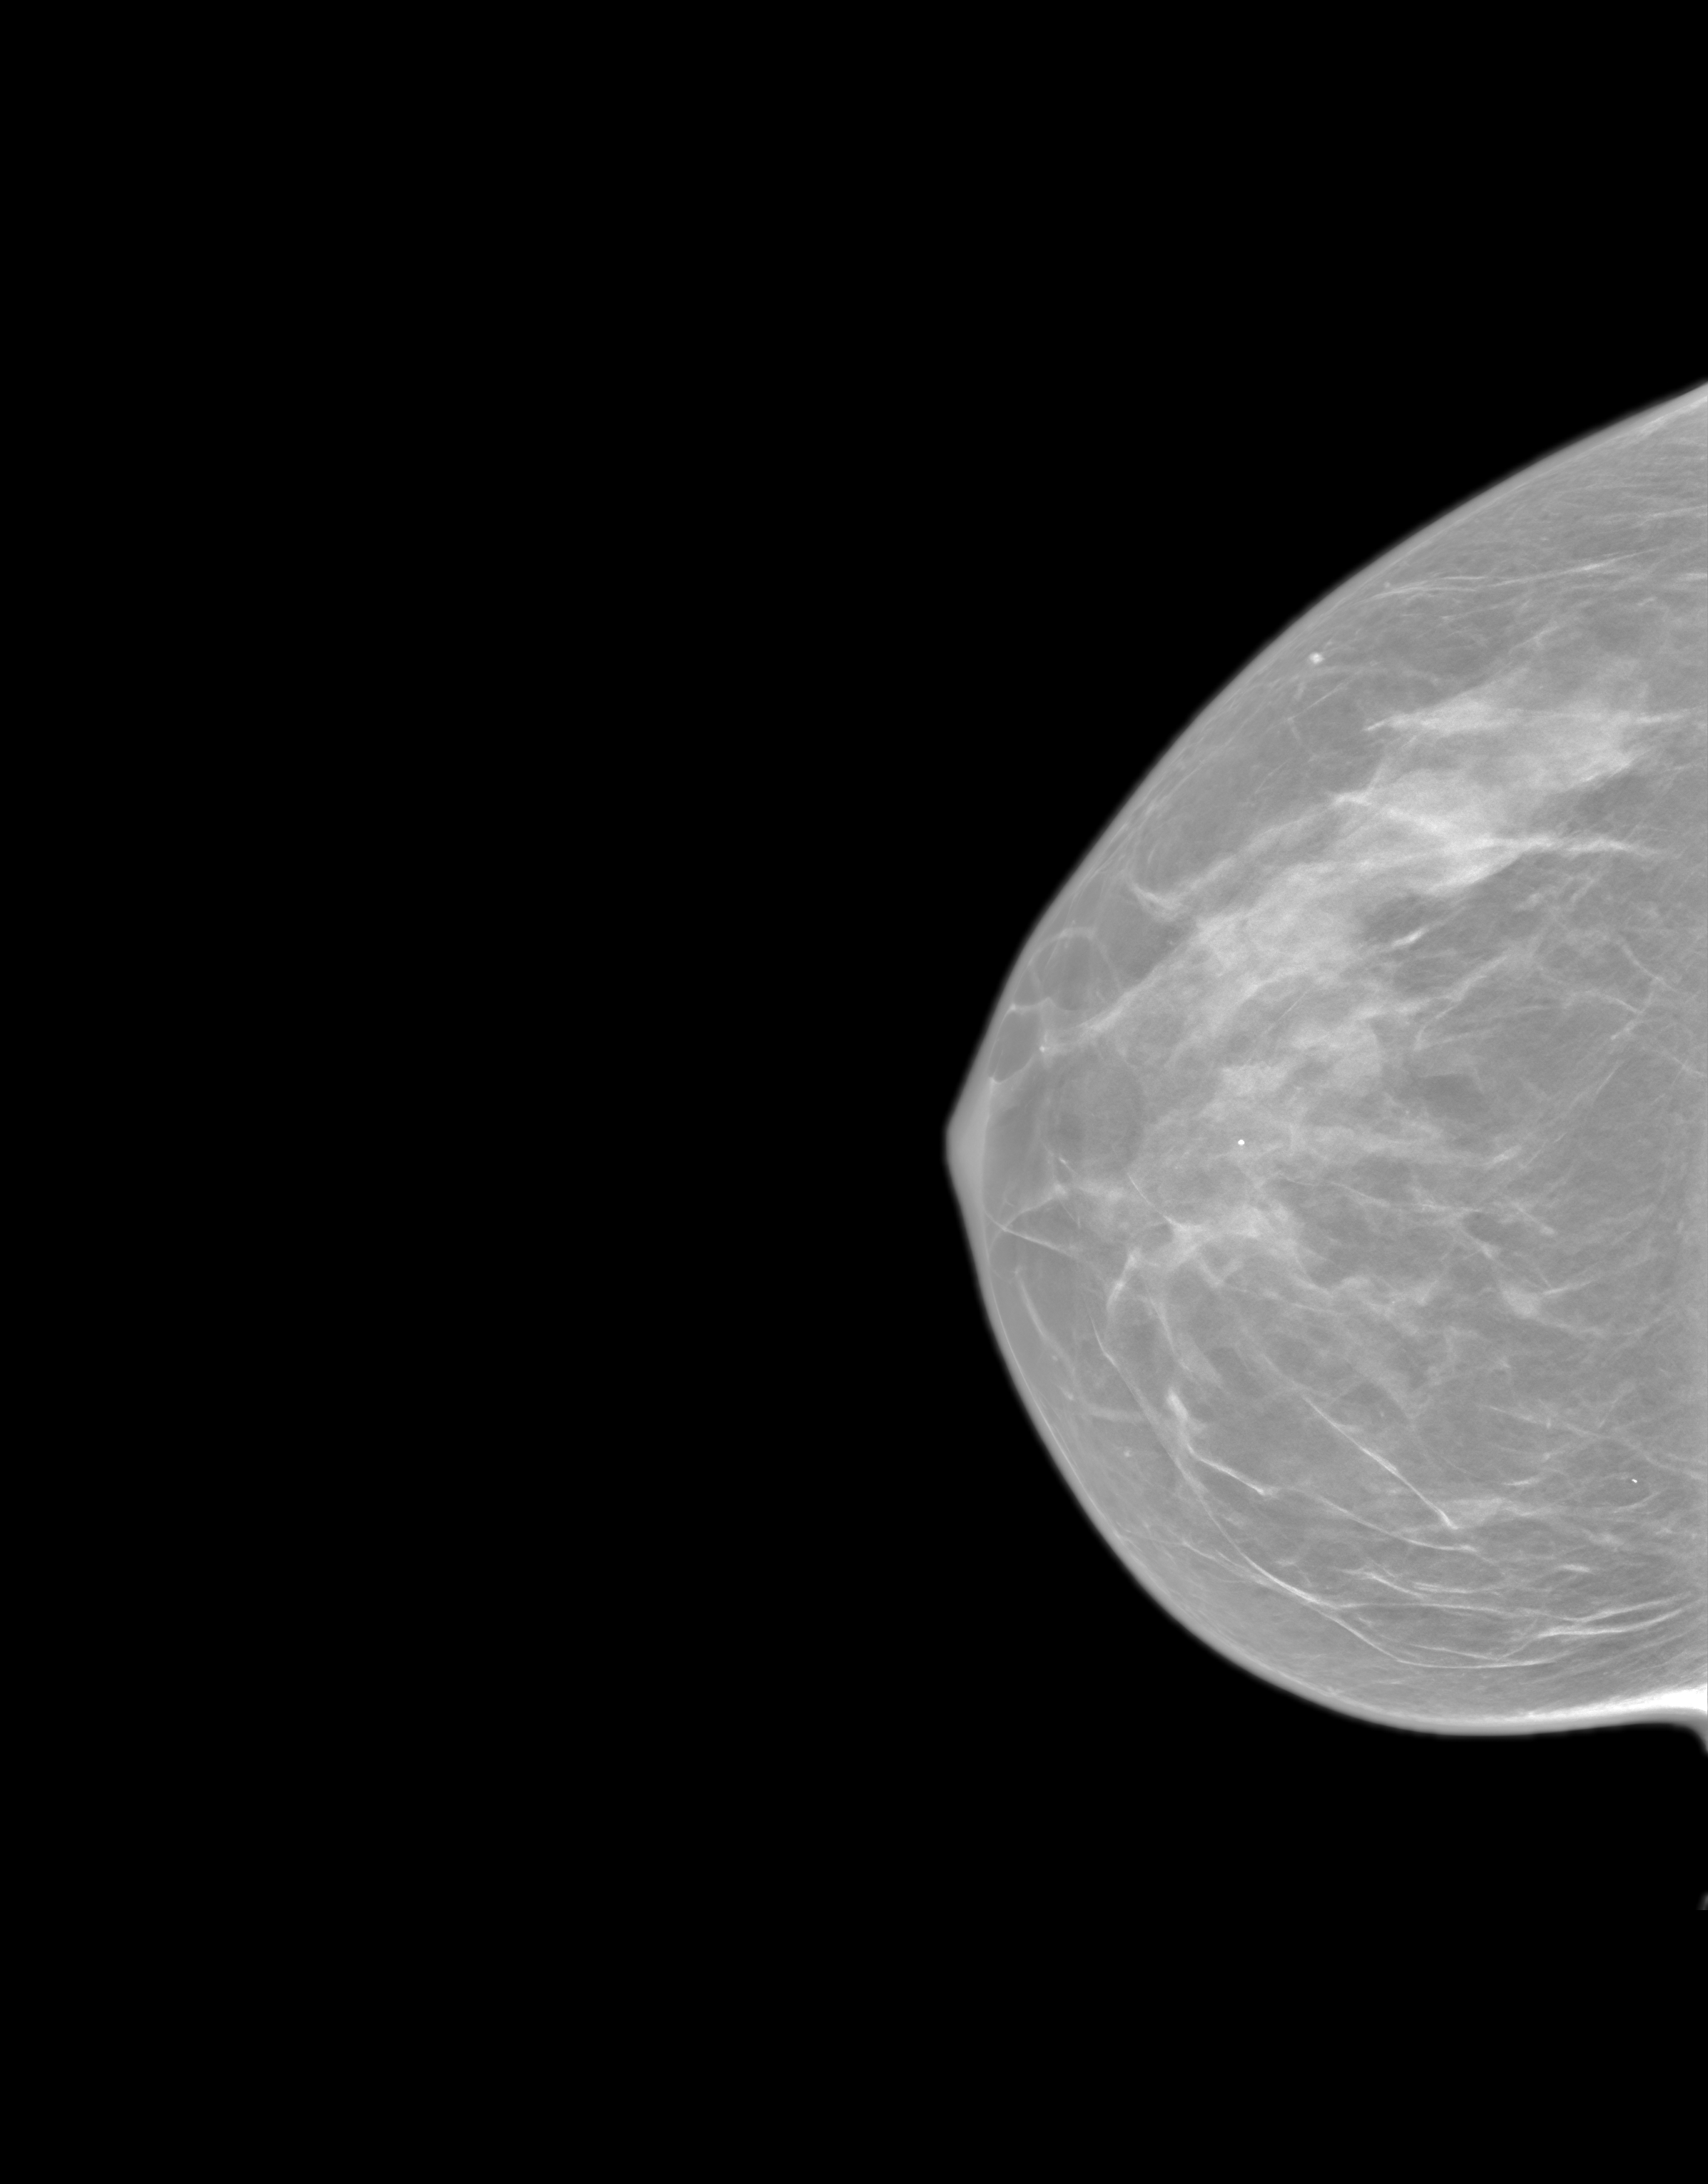
Synthesized 2-D mammogram reconstructed from digital breast tomosynthesis; right breast; craniocaudal (CC) view; screening examination; system: SenoIris_1SP1.2(425). Female patient, age 51 years.
BI-RADS breast density category at the screening exam (both breasts, scale 1–4): 3. Final BI-RADS assessment for this screening round (tomosynthesis exam, both breasts): category 2. Recall: no recall after this screen.